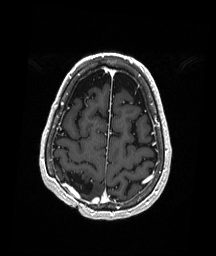
Brain MRI from a brain-tumour surgery series, one axial slice. T1-weighted post-contrast. 216 × 256 image matrix, field of view 211 × 250 mm. Case-level facts recorded for this patient, not image findings: histopathology: Astrocytoma; WHO grade: 3; IDH mutation: yes; tumour location: Right Parietal.
Outlined on this slice (outlined manually by an expert reader):
- previous resection cavity: bounding box [x1, y1, x2, y2] px = [62, 172, 93, 195]